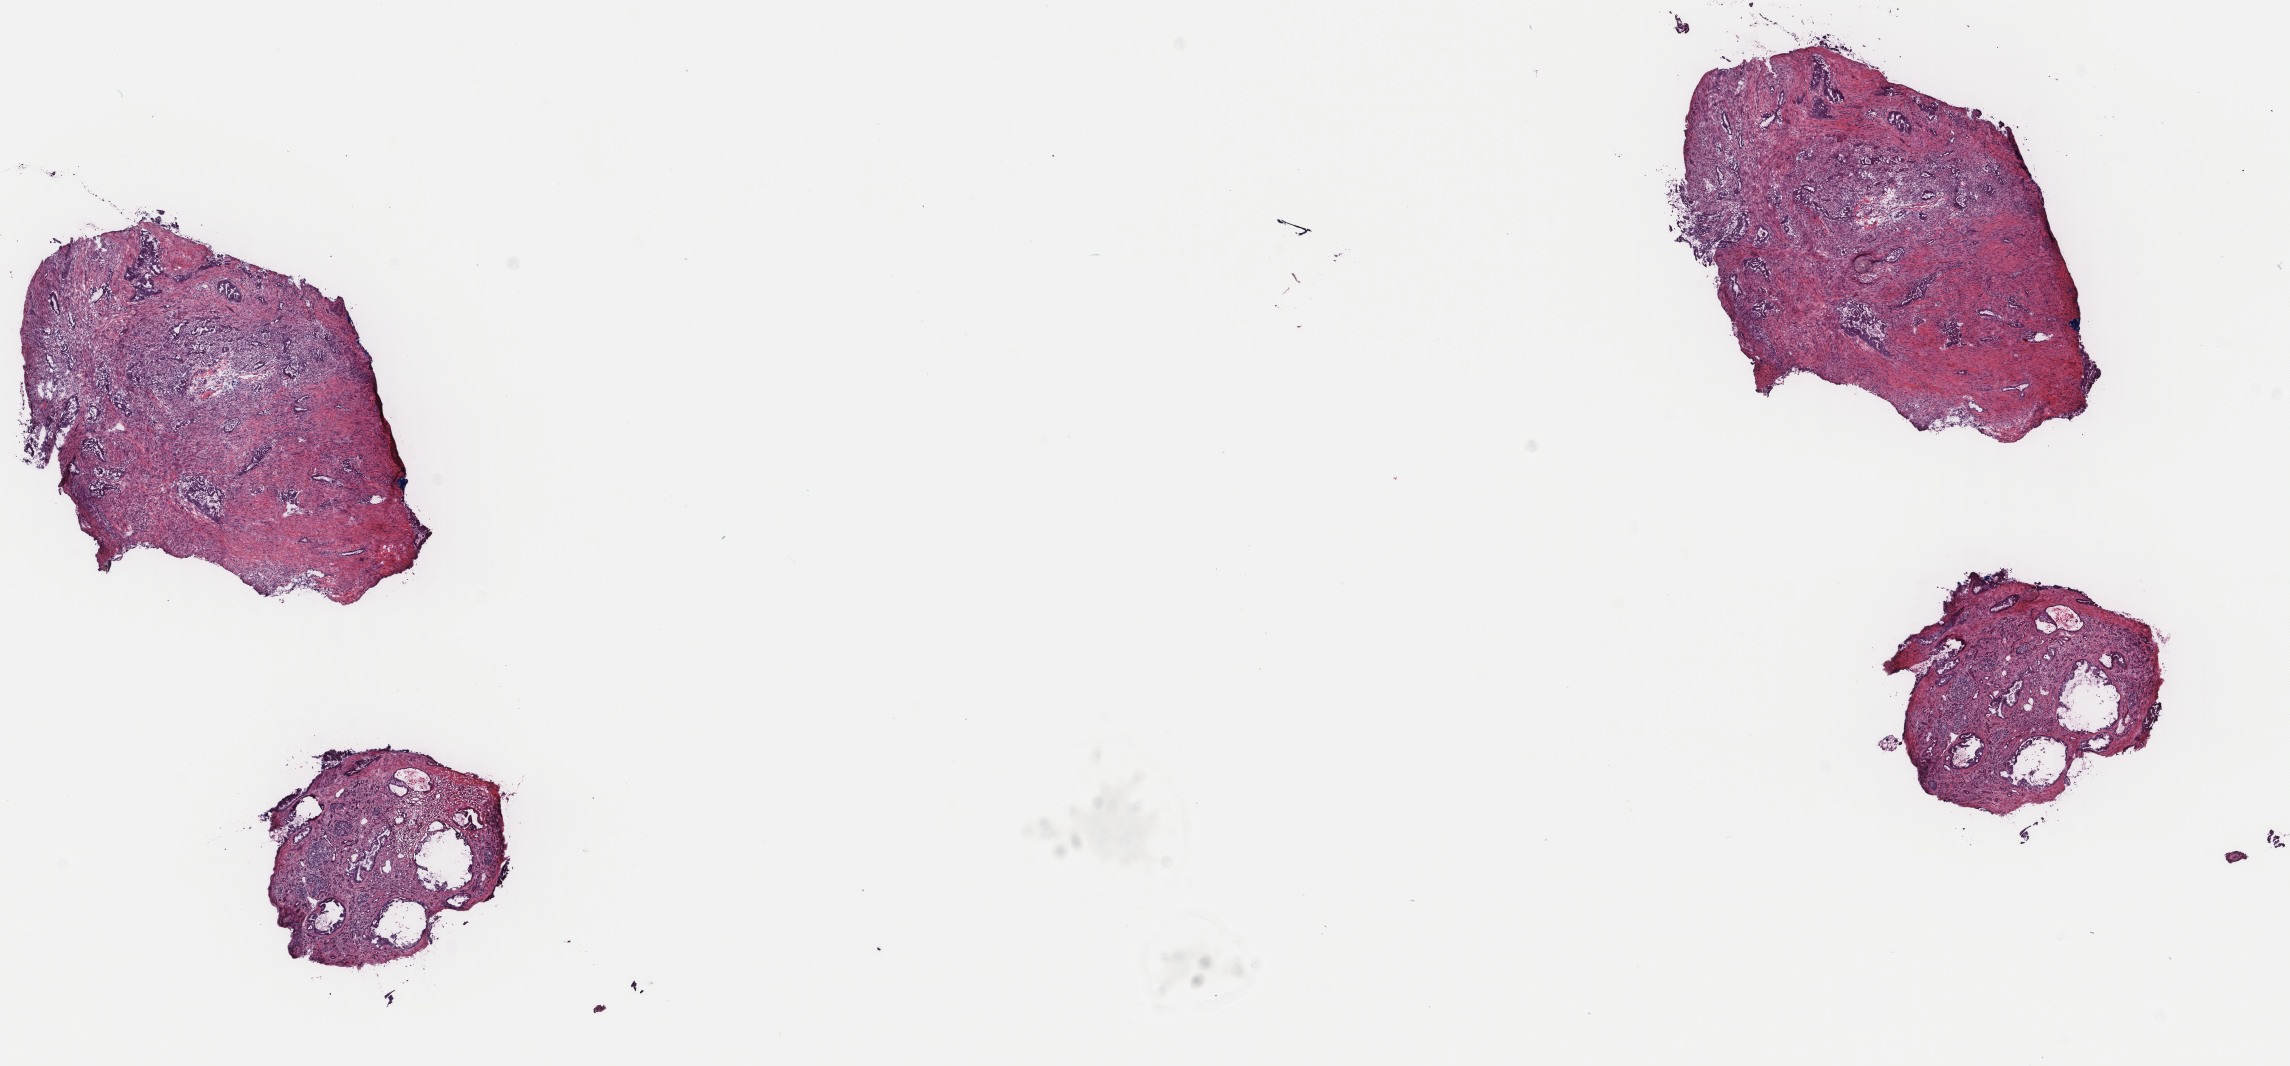
Whole-slide histology image, Hematoxylin and eosin (H&E) stained — a low-resolution overview of the entire scanned area, about 18.2 x 8.5 mm, frozen section, pancreas, primary tumour sample. Male, age 65 years at initial diagnosis. Histologic grade: G2 (moderately differentiated). Composition of this section per pathologist review: tumour cells 100%, tumour nuclei 35%, normal cells 0%, stromal cells 0%, necrosis 0%. Infiltration values recorded for this section: lymphocyte infiltration 5%, monocyte infiltration 0%, neutrophil infiltration 0%.
Lymph nodes positive (case pathology): 0 of 8 examined. Pathologic diagnosis: Adenocarcinoma, NOS (head of pancreas). AJCC pathologic stage: IIA (7th edition).